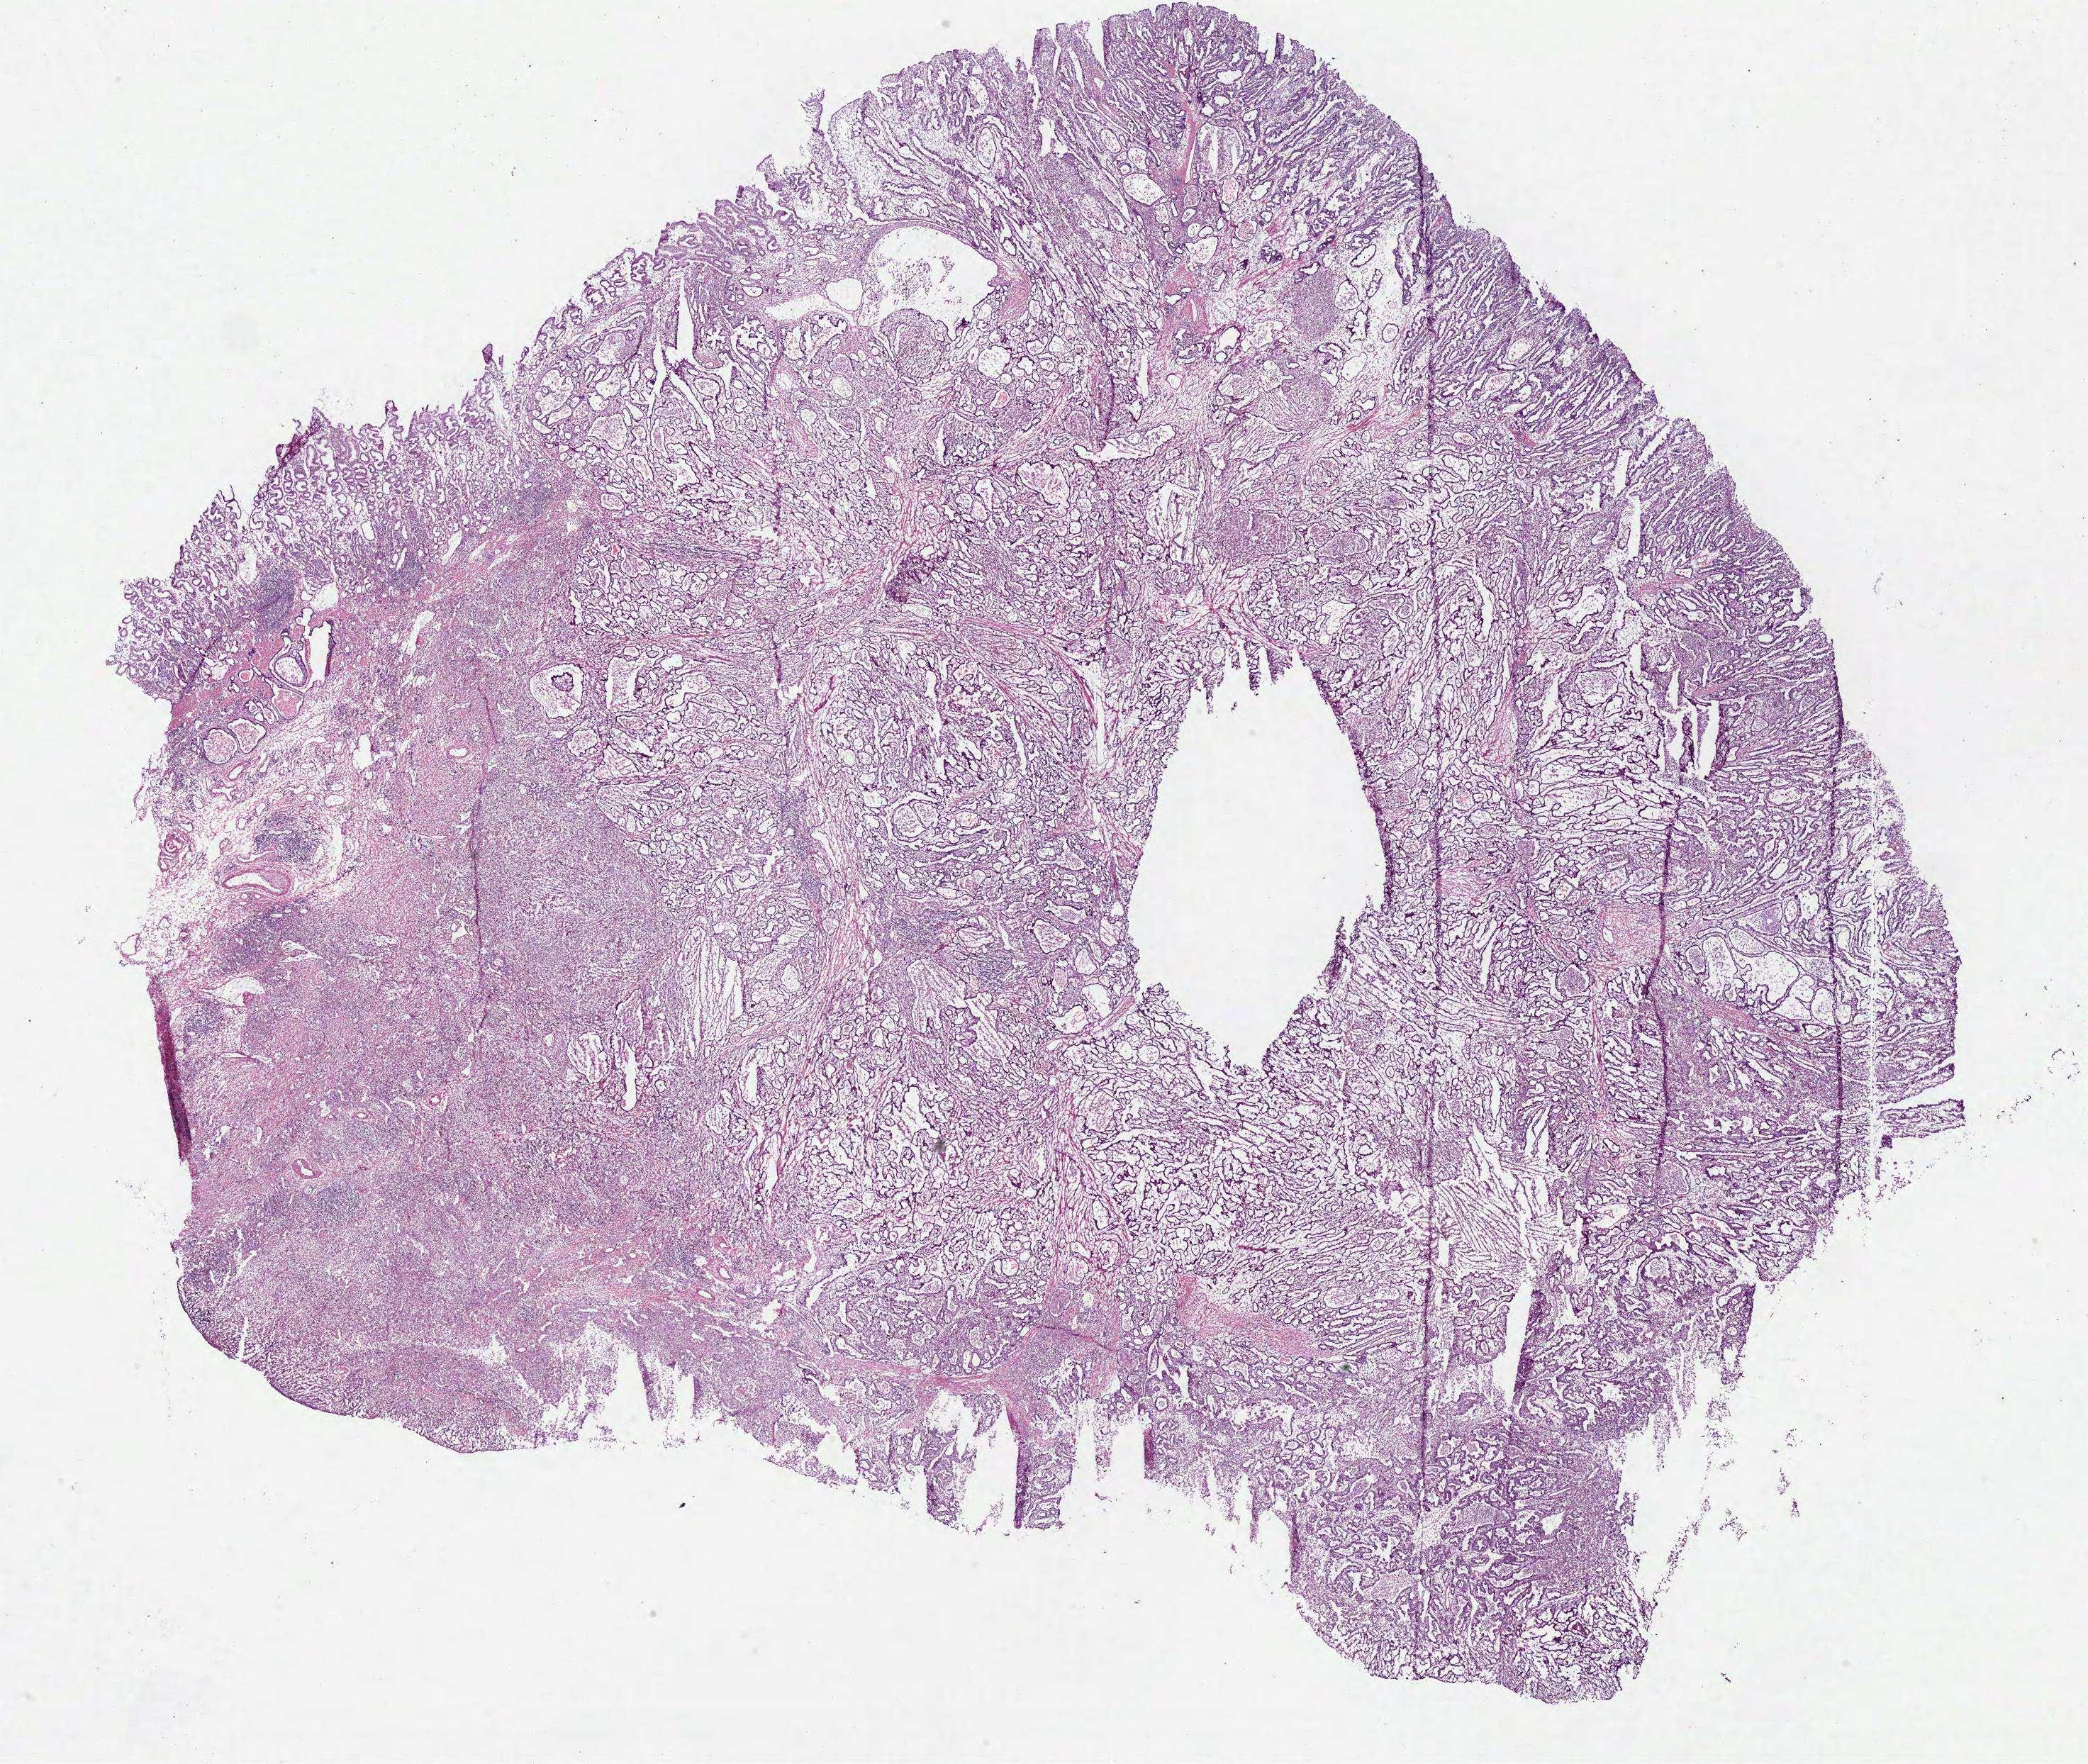
Hematoxylin and eosin (H&E) stained whole-slide image — a low-resolution overview of the entire scanned area, about 23.2 x 19.6 mm. Frozen section. Primary tumour sample from the stomach. Male patient; age at initial diagnosis 41 years. Histologic grade: G2 (moderately differentiated). Pathologist review of this section (percent, as recorded): tumour cells 70%, tumour nuclei 70%, normal cells 5%, stromal cells 20%, necrosis 5%.
Pathologic diagnosis: Adenocarcinoma, NOS. Lymph nodes positive (case pathology): 0 of 15 examined. AJCC pathologic stage: IB. TNM: T2 N0 M0.